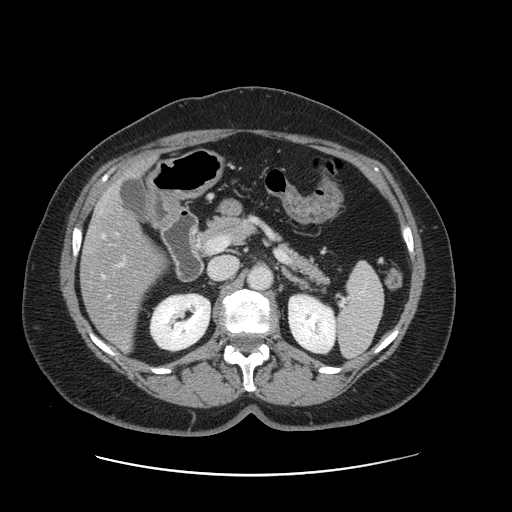
Contrast-enhanced abdominal CT, one axial slice. Slice 72 of 161 in the series (ordered by position). 120 kVp. Intravenous contrast given. Soft-tissue window (W 400 / L 40 HU). 2.5 mm slice thickness. 512 × 512 image matrix, field of view 398 × 398 mm. Female patient, age 62 years. Case-level facts recorded for this patient, not image findings: diagnosis: colorectal cancer liver metastases, imaged before liver resection; multiple liver metastases: no.
Structures marked on this image (outlined manually by an expert reader):
- hepatic veins: box from (x=102, y=234) to (x=110, y=298) px
- liver: (x=82, y=165)–(x=165, y=350)
- planned liver remnant (the part of the liver to remain after resection): (x=134, y=165)–(x=146, y=173)
- portal vein (with intrahepatic branches): (x=116, y=233)–(x=120, y=266)